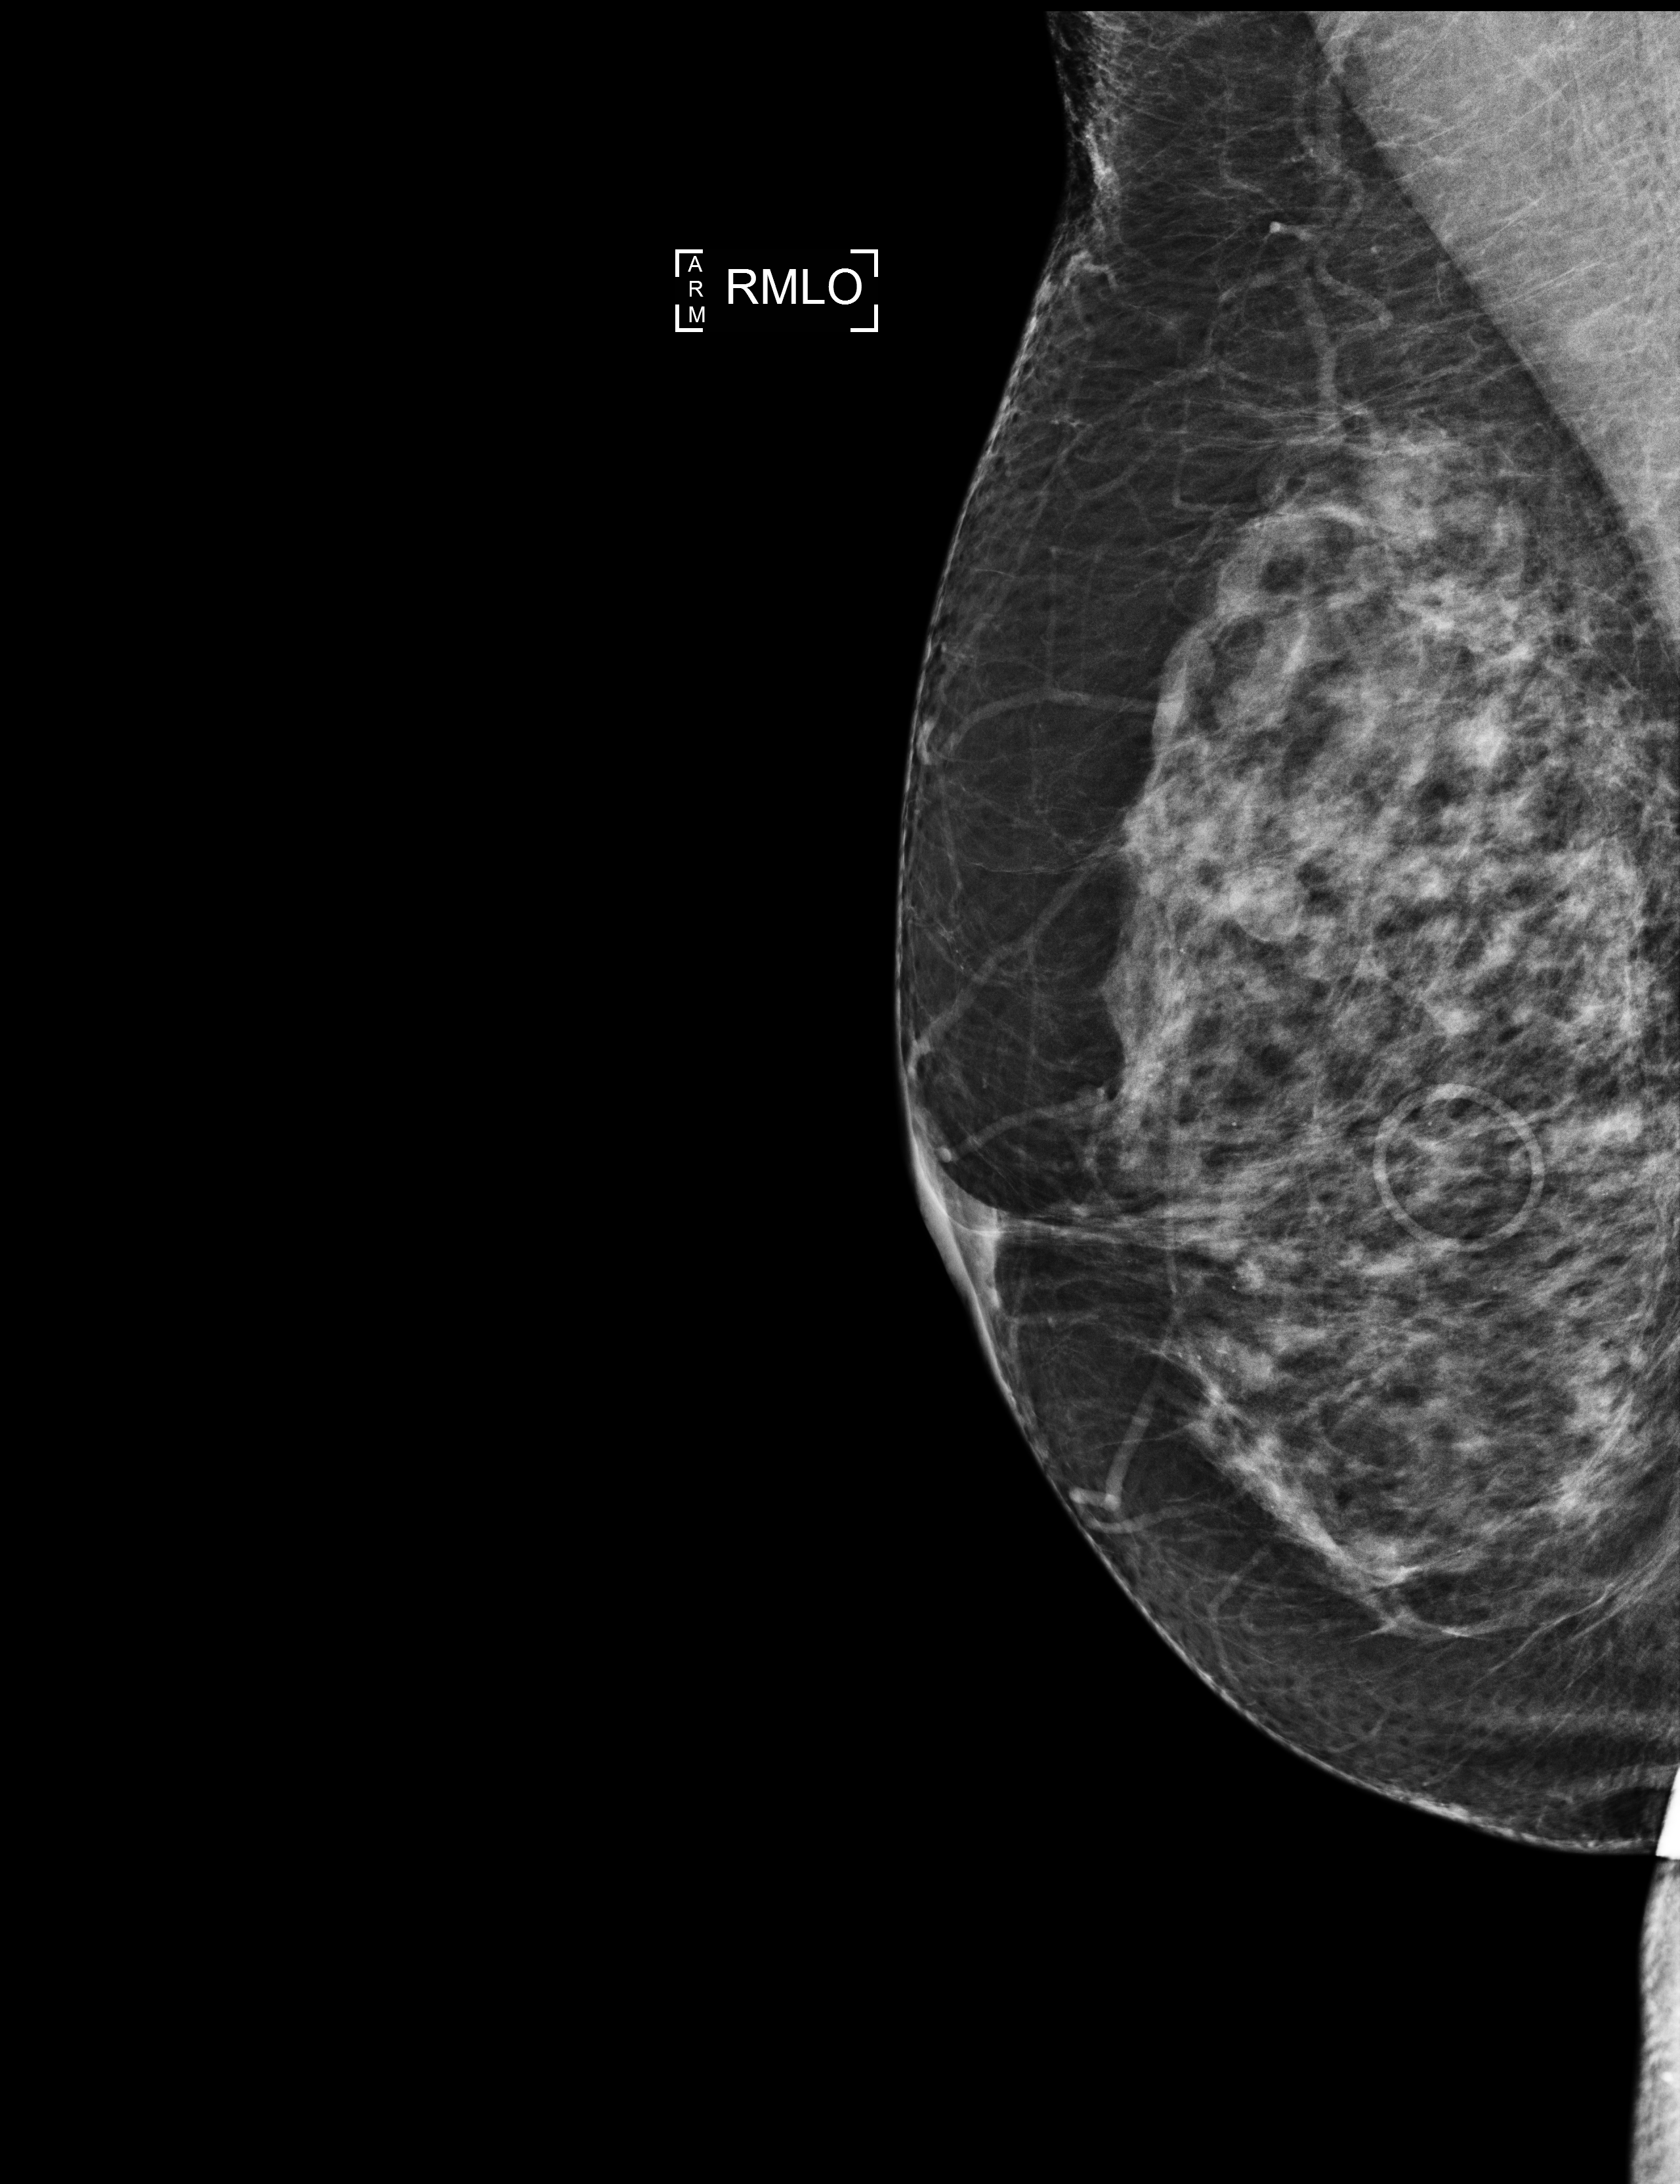
Screening examination, system: Selenia Dimensions.
Image type: full-field digital mammogram. Breast: right. Projection: MLO view.